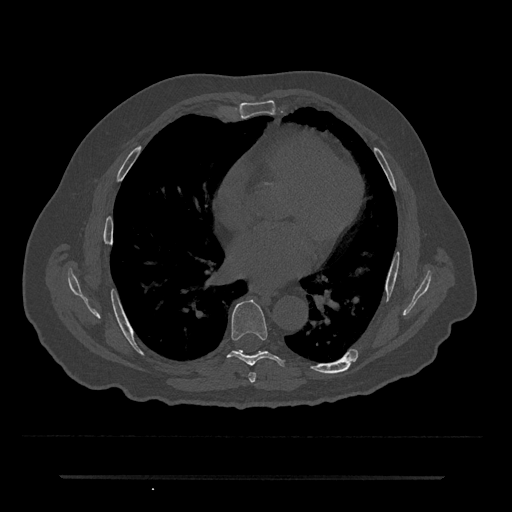
CT including the spine, one axial slice. Slice 382 of 797 in the series (ordered by position). 120 kVp. Bone window (W 1800 / L 400 HU). 0.5 mm slice thickness. 512 × 512 image matrix, field of view 437 × 437 mm. Male patient, age 69 years. From the clinical record (not read from this slice): primary cancer: prostate.
Outlined on this slice (semi-automatic segmentation, software-assisted and operator-edited):
- T6 vertebra: bounding box <249,372,256,383> (left, top, right, bottom; pixels)
- T7 vertebra: <228,300,286,366>